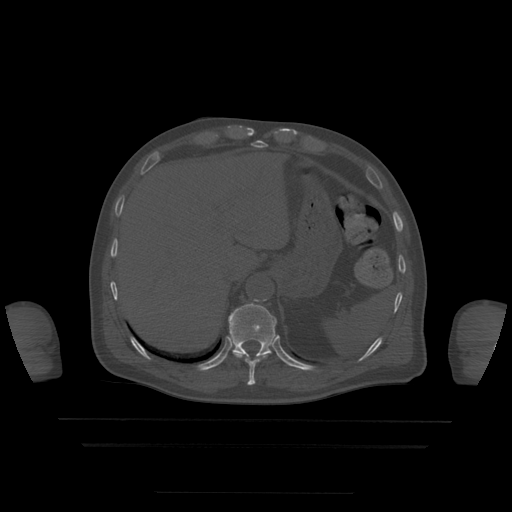
CT including the spine, one axial slice. Slice 229 of 522 in the series (ordered by position). Bone window (W 1800 / L 400 HU). 512 × 512 image matrix, field of view 436 × 436 mm. Patient age 68 years. From the clinical record (not read from this slice): primary cancer: urothelial.
Structures marked on this image (semi-automatically segmented with operator editing):
- T10 vertebra: bounding box (x1, y1, x2, y2) in pixels: (233, 351, 267, 386)
- T11 vertebra: (228, 304, 277, 357)